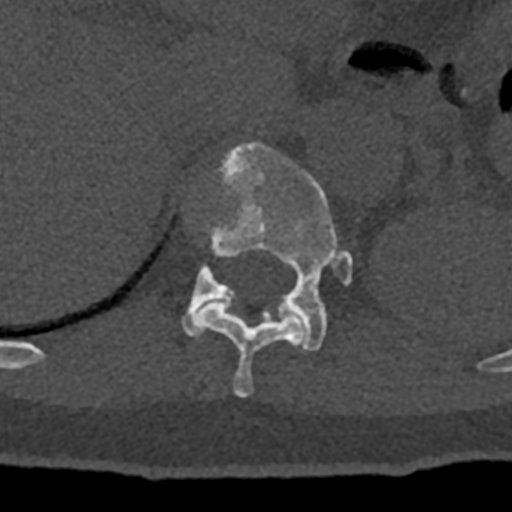
CT including the spine, one axial slice. Position 519 of 797 along the scan axis. 120 kVp. Bone window (W 1800 / L 400 HU). 0.5 mm slice thickness. 512 × 512 image matrix, field of view 160 × 160 mm. Male patient, age 74 years. Case-level facts recorded for this patient, not image findings: primary cancer: renal.
Outlined on this slice (semi-automatically segmented with operator editing):
- T11 vertebra: bounding box [x1, y1, x2, y2] px = [193, 301, 307, 398]
- T12 vertebra: [181, 142, 353, 351]